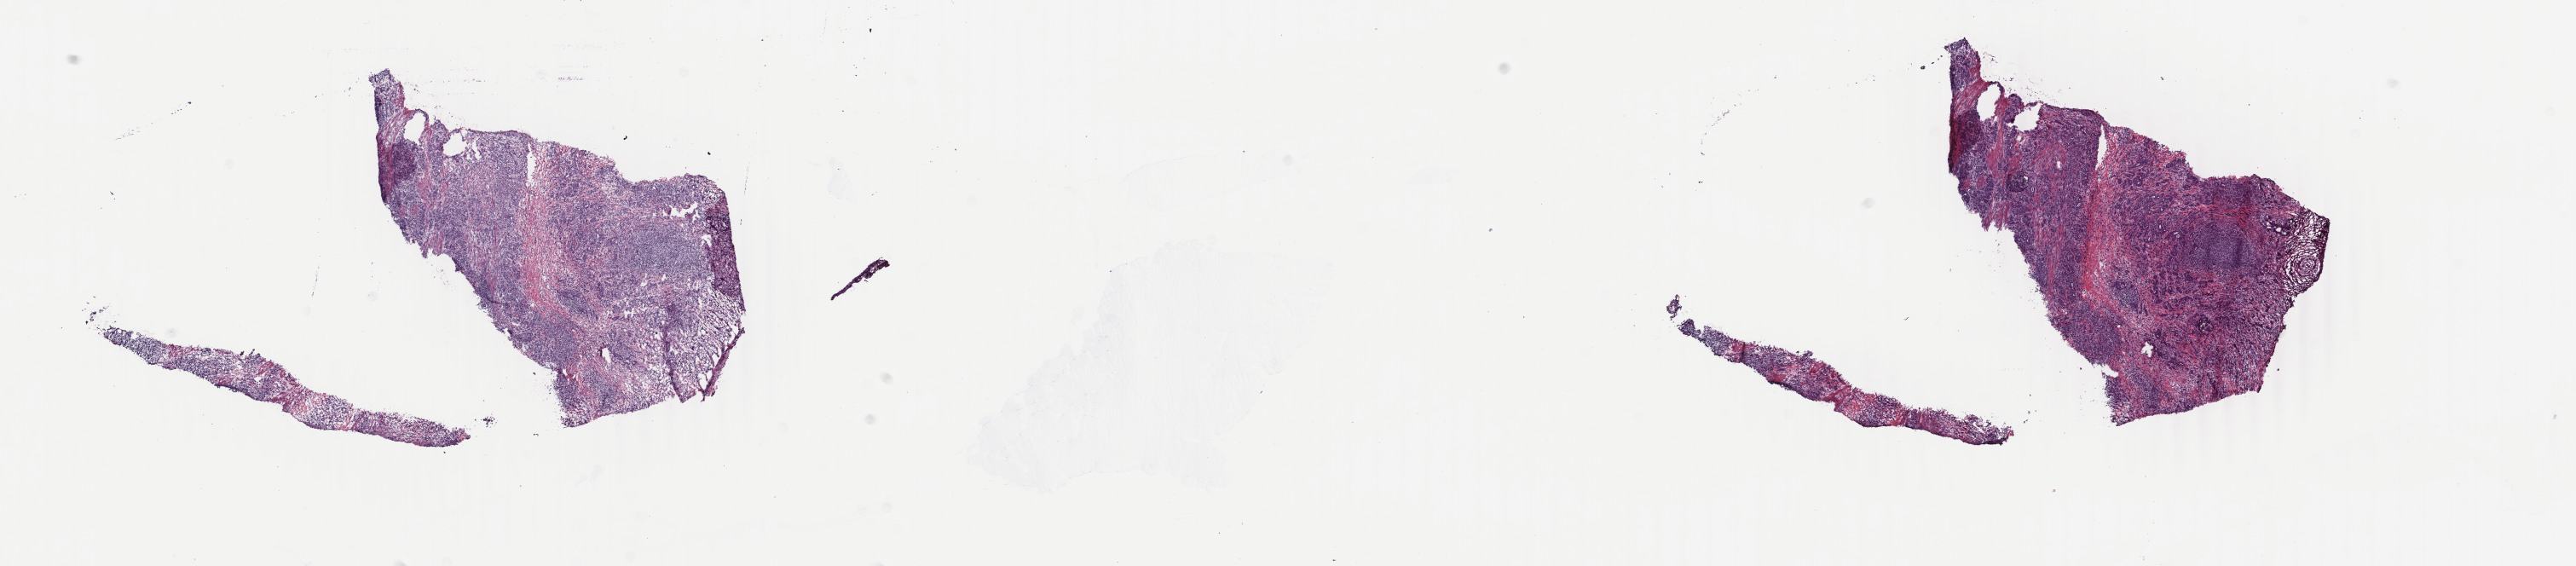
Whole-slide histology image, H&E, low-resolution overview of the scanned area, about 24.0 x 5.3 mm. Frozen section from the top of the tissue portion. Sample: primary tumour, stomach. Patient: male, age at initial diagnosis 73 years. Composition of this section per pathologist review: tumour cells 40%, tumour nuclei 60%.
Pathologic diagnosis: Tubular adenocarcinoma (fundus of stomach).